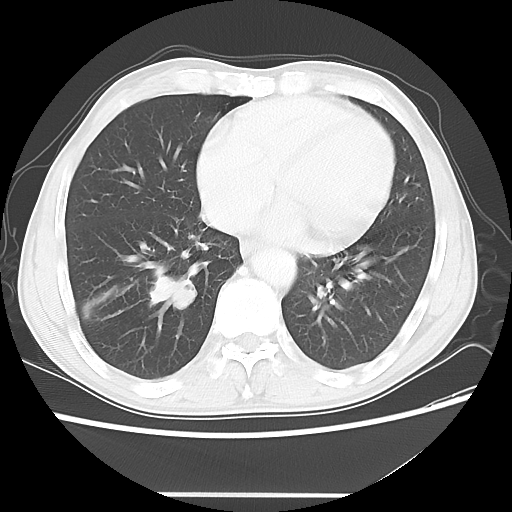
Chest CT, one axial slice; slice 18 of 56 in the series (ordered by position); reconstruction kernel LUNG; 120 kVp; lung window (W 1500 / L -600 HU); 512 × 512 image matrix, field of view 344 × 344 mm. Male patient, age 65 years. Case-level facts recorded for this patient, not image findings: clinical TNM (as recorded): T1c N3 M0; histopathological grade: G3.
Outlined on this slice (rectangle marked by the reading radiologist):
- lung tumour (recorded histology: small cell carcinoma): bounding box <145,271,202,312> (left, top, right, bottom; pixels)